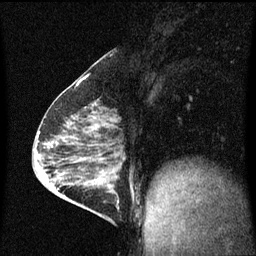
Breast MRI (dynamic contrast-enhanced), one sagittal slice. Dynamic contrast-enhanced series, image 2 of 3 at this slice position (ordered by acquisition). 1.5 T. TE 4.2 ms, TR 8 ms. 256 × 256 image matrix. Female patient, age 64 years.
Annotated regions visible in this slice (semi-automatic segmentation, software-assisted and operator-edited):
- analysis volume of interest (the breast-tissue region the enhancement analysis was run in; not a lesion): box from (x=87, y=176) to (x=120, y=217) px
- tumour enhancement mask (voxels above the 70 % enhancement threshold inside the analysis volume of interest): (x=97, y=180)–(x=115, y=195)